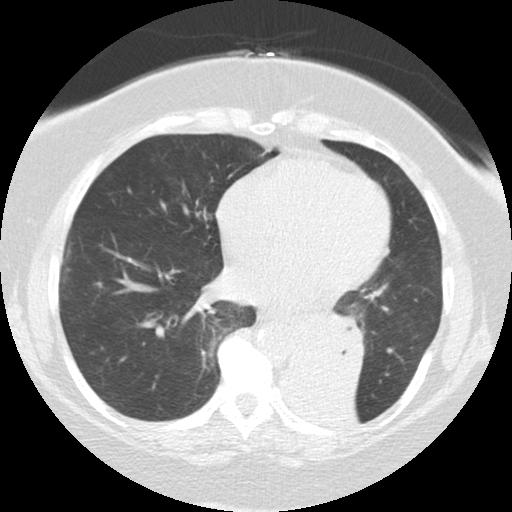
Chest CT (low-dose screening protocol), one axial image; baseline annual screen; lung window (W 1500 / L -600 HU); 120 kVp; slice 77 of 136 in the series. Female, age 71 years at enrolment. Former smoker at enrolment.
Lesion marked by an expert reader, bounding box <280,303,369,384> (left, top, right, bottom; pixels). The exam's reader record, not a measurement of the box and not confirmed to be the same lesion: non-calcified nodule or mass ≥4 mm, right middle lobe, 5 × 5 mm, smooth margins, soft tissue attenuation. Note: the box lies in the patient's left hemithorax on this image, whereas the reader's record names the right lung; they may be different findings. Participant outcome: lung cancer diagnosed 46 days after this screen — large cell carcinoma, NOS, left lower lobe, mediastinum, other location, poorly differentiated (G3), stage IV (AJCC 6th edition), 50 mm at pathology.